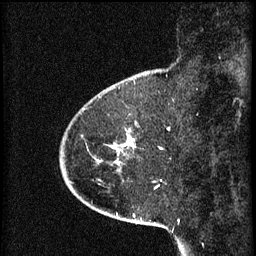
Breast MRI (dynamic contrast-enhanced), one sagittal slice. Position 14 of 60 along the scan axis. 3 images stored at this slice position (order not interpretable as contrast timing). 1.5 T. TE 4.2 ms, TR 8.2 ms. 2 mm slice thickness. 256 × 256 image matrix, field of view 200 × 200 mm. Female patient, age 45 years.
Outlined on this slice (semi-automatically segmented with operator editing):
- analysis volume of interest (the breast-tissue region the enhancement analysis was run in; not a lesion): bounding box <80,102,138,165> (left, top, right, bottom; pixels)
- tumour enhancement mask (voxels above the 70 % enhancement threshold inside the analysis volume of interest): <111,136,134,149>